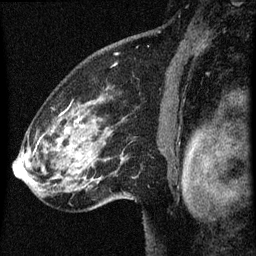
Breast MRI (dynamic contrast-enhanced), one sagittal slice; position 46 of 60 along the scan axis; dynamic contrast-enhanced series, image 2 of 3 at this slice position (ordered by acquisition); 1.5 T; TE 4.2 ms, TR 8 ms; 2 mm slice thickness; 256 × 256 image matrix, field of view 180 × 180 mm. Patient: female, 61 years.
Annotated regions visible in this slice (semi-automatically segmented with operator editing):
- analysis volume of interest (the breast-tissue region the enhancement analysis was run in; not a lesion): bounding box (x1, y1, x2, y2) in pixels: (27, 86, 134, 209)
- tumour enhancement mask (voxels above the 70 % enhancement threshold inside the analysis volume of interest): (34, 110, 79, 153)